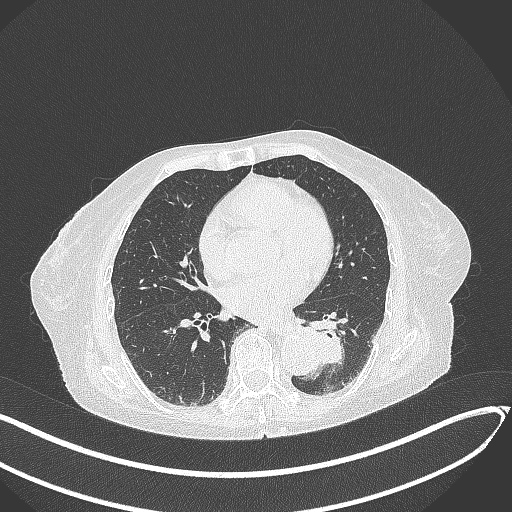
Chest CT, one axial slice; position 106 of 324 along the scan axis; reconstruction kernel B70f; lung window (W 1500 / L -600 HU); 512 × 512 image matrix, field of view 400 × 400 mm. Female patient, age 82 years. Case-level facts recorded for this patient, not image findings: clinical TNM (as recorded): T1b N0 M1.
Outlined on this slice (bounding box drawn by a radiologist):
- lung tumour (recorded histology: adenocarcinoma): bounding box (x1, y1, x2, y2) in pixels: (294, 319, 350, 368)